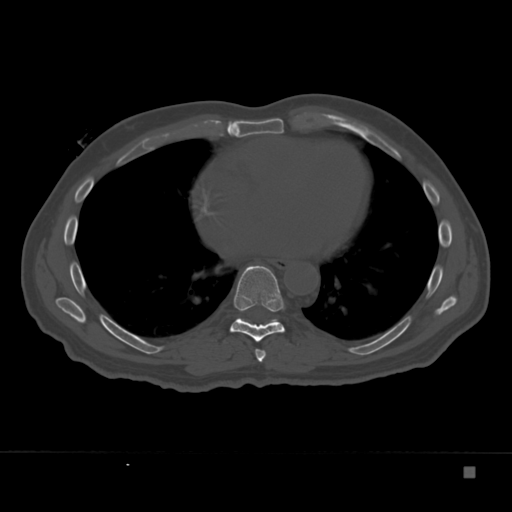
CT including the spine, one axial slice. Slice 206 of 332 in the series (ordered by position). 120 kVp. Bone window (W 1800 / L 400 HU). 512 × 512 image matrix. Patient: male, 72 years. From the clinical record (not read from this slice): primary cancer: skeletal.
Outlined on this slice (semi-automatic segmentation, software-assisted and operator-edited):
- T7 vertebra: box from (x=255, y=349) to (x=266, y=362) px
- T8 vertebra: (x=230, y=265)–(x=285, y=342)
- T9 vertebra: (x=239, y=318)–(x=278, y=323)